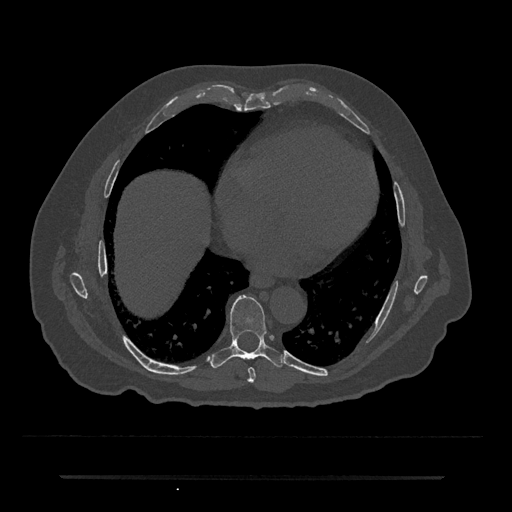
CT including the spine, one axial slice; slice 340 of 797 in the series (ordered by position); reconstruction kernel Br40s/3; bone window (W 1800 / L 400 HU); 0.5 mm slice thickness; 512 × 512 image matrix, field of view 437 × 437 mm. Patient: male, 69 years. Case-level facts recorded for this patient, not image findings: primary cancer: prostate.
Annotated regions visible in this slice (semi-automatic segmentation, software-assisted and operator-edited):
- T7 vertebra: bounding box <248,367,256,383> (left, top, right, bottom; pixels)
- T8 vertebra: <211,295,283,368>